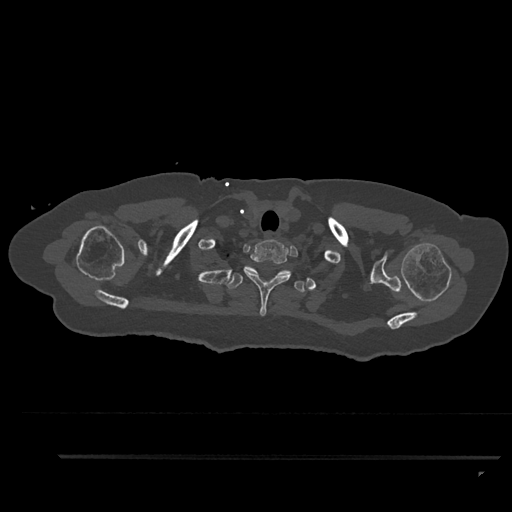
CT including the spine, one axial slice; slice 749 of 797 in the series (ordered by position); 120 kVp; bone window (W 1800 / L 400 HU); 0.5 mm slice thickness; 512 × 512 image matrix, field of view 408 × 408 mm. Female patient, age 44 years. From the clinical record (not read from this slice): primary cancer: renal; vertebrae with lytic lesions (as recorded): L1.
Annotated regions visible in this slice (semi-automatically segmented with operator editing):
- T1 vertebra: bounding box <241,239,291,316> (left, top, right, bottom; pixels)
- T2 vertebra: <227,268,305,293>